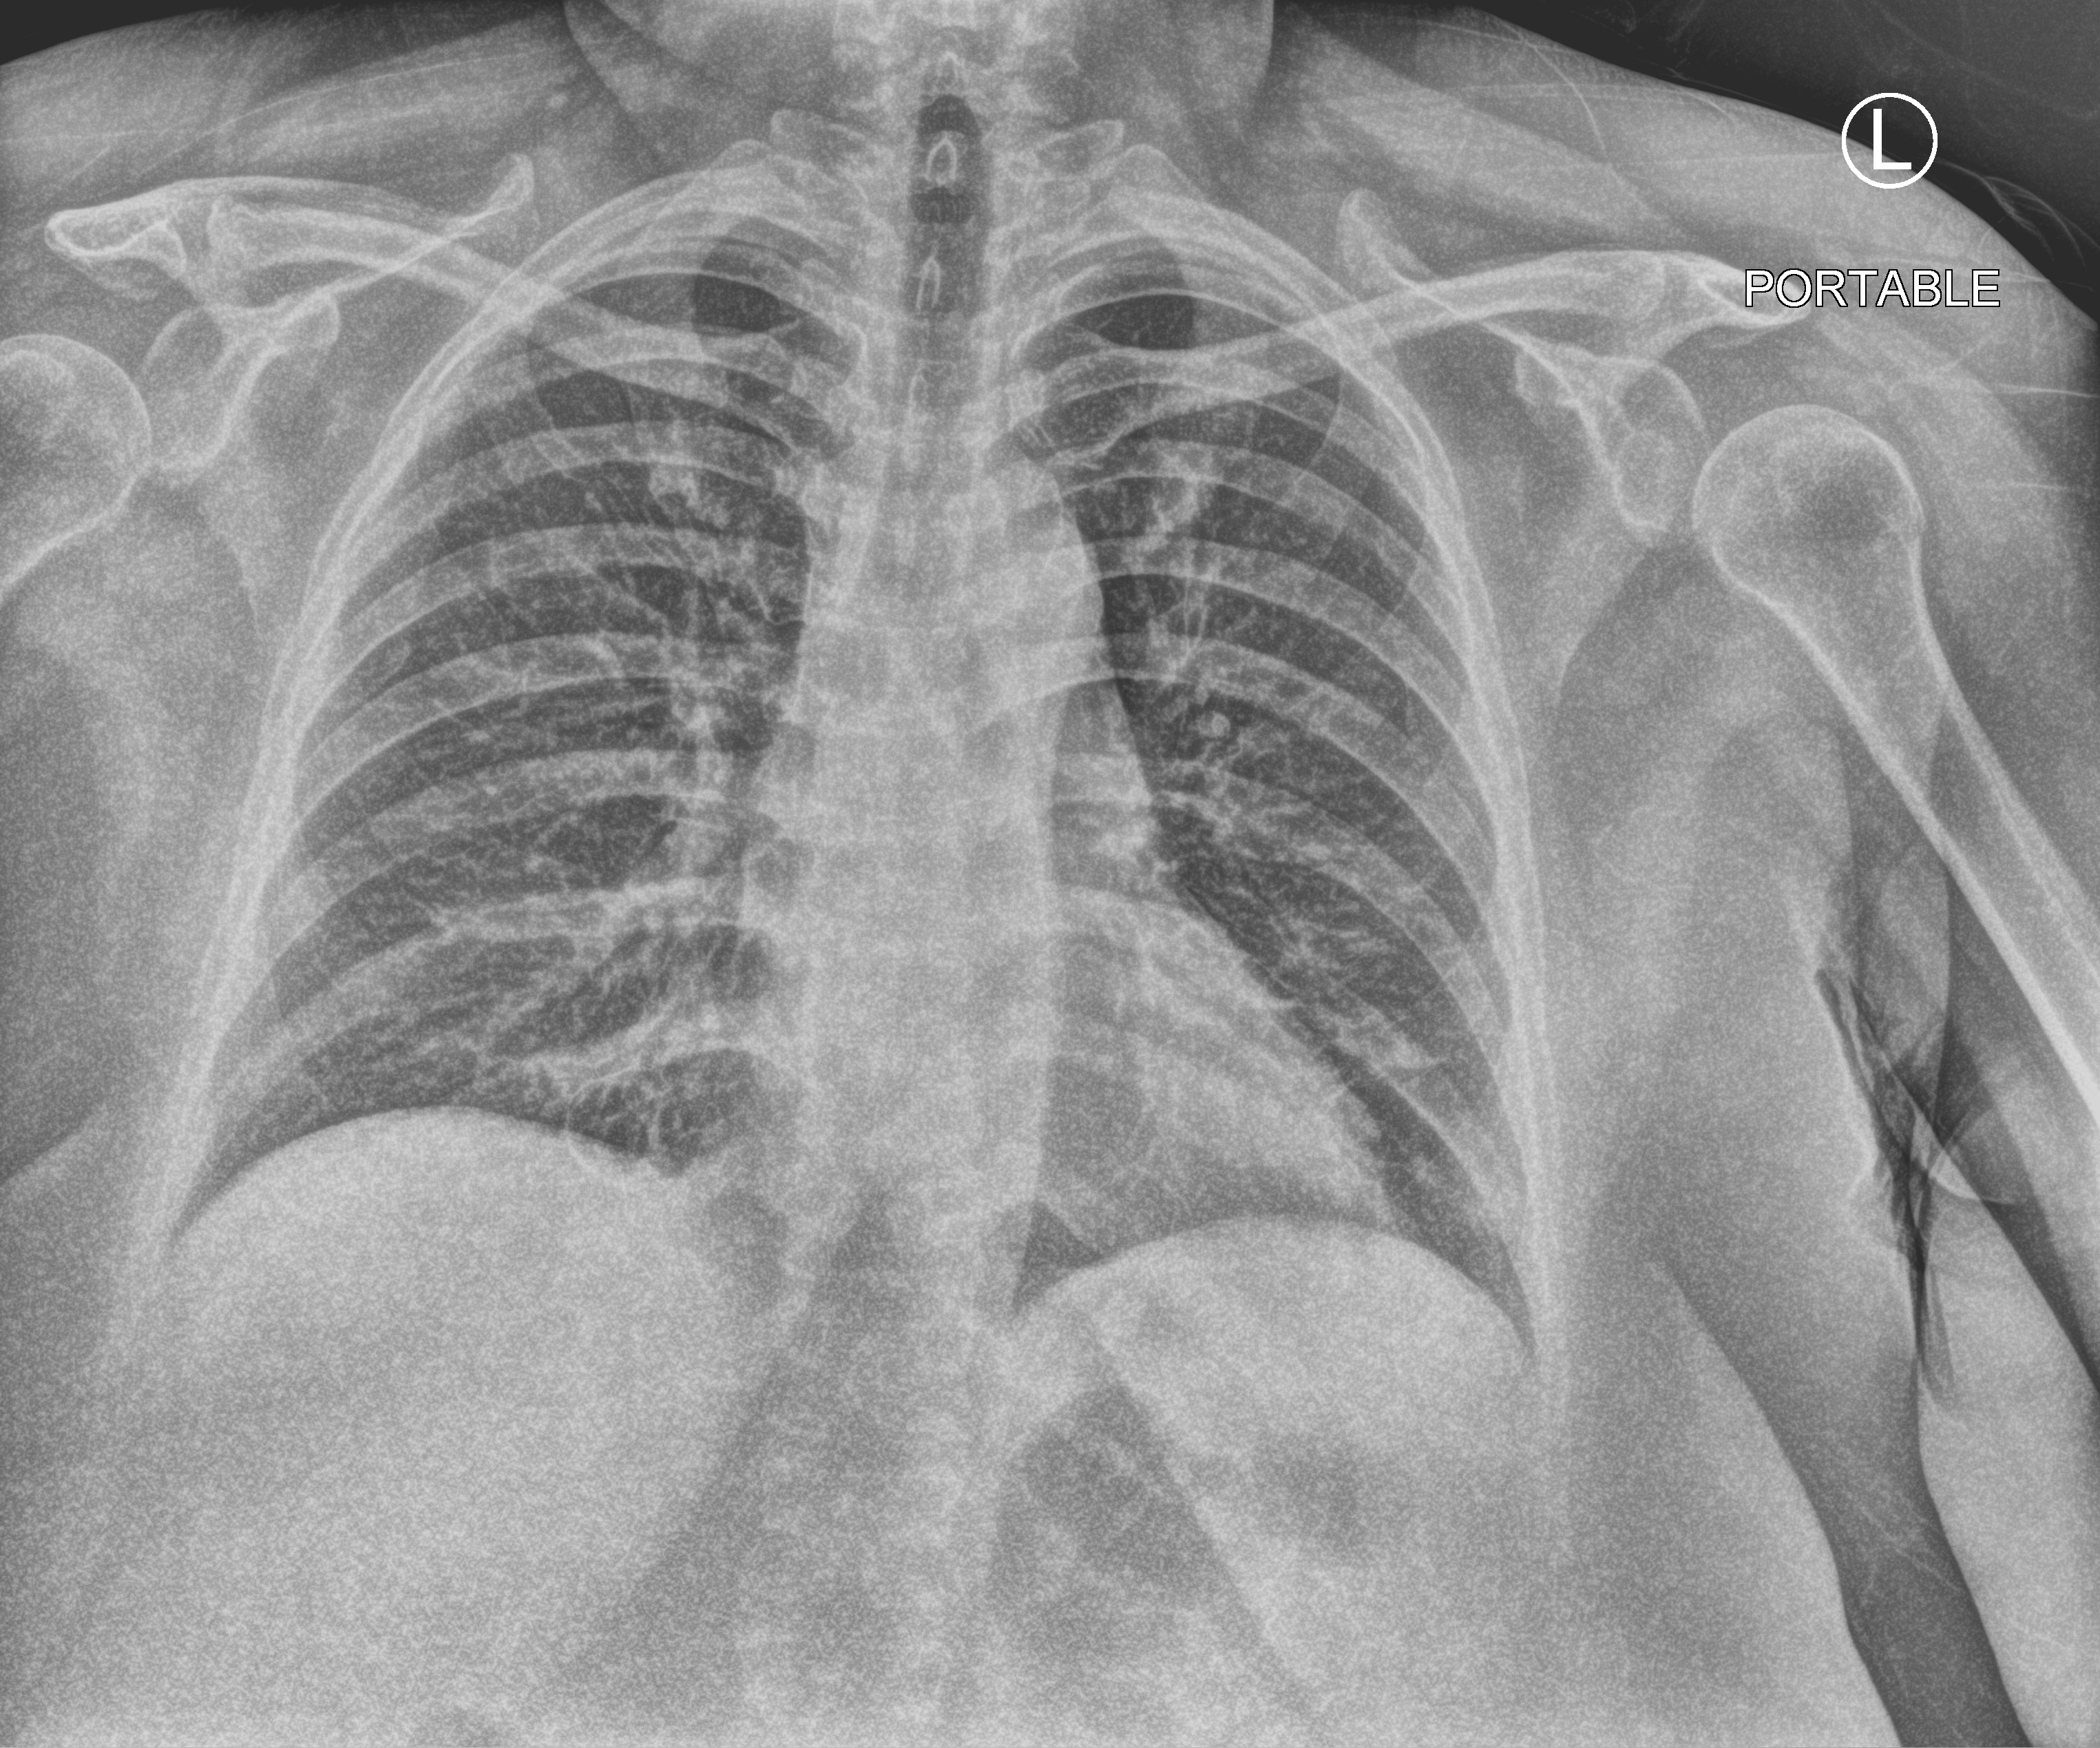
Bedside chest radiograph (computed radiography); anteroposterior (AP) projection. Patient hospitalised with COVID-19; female, aged 18–59 years.
Admission-level facts for this patient (not findings on this image; timing relative to this image not recorded): admitted to intensive care during this hospital stay: no; hypertension (admission record): yes; diabetes (admission record): yes.